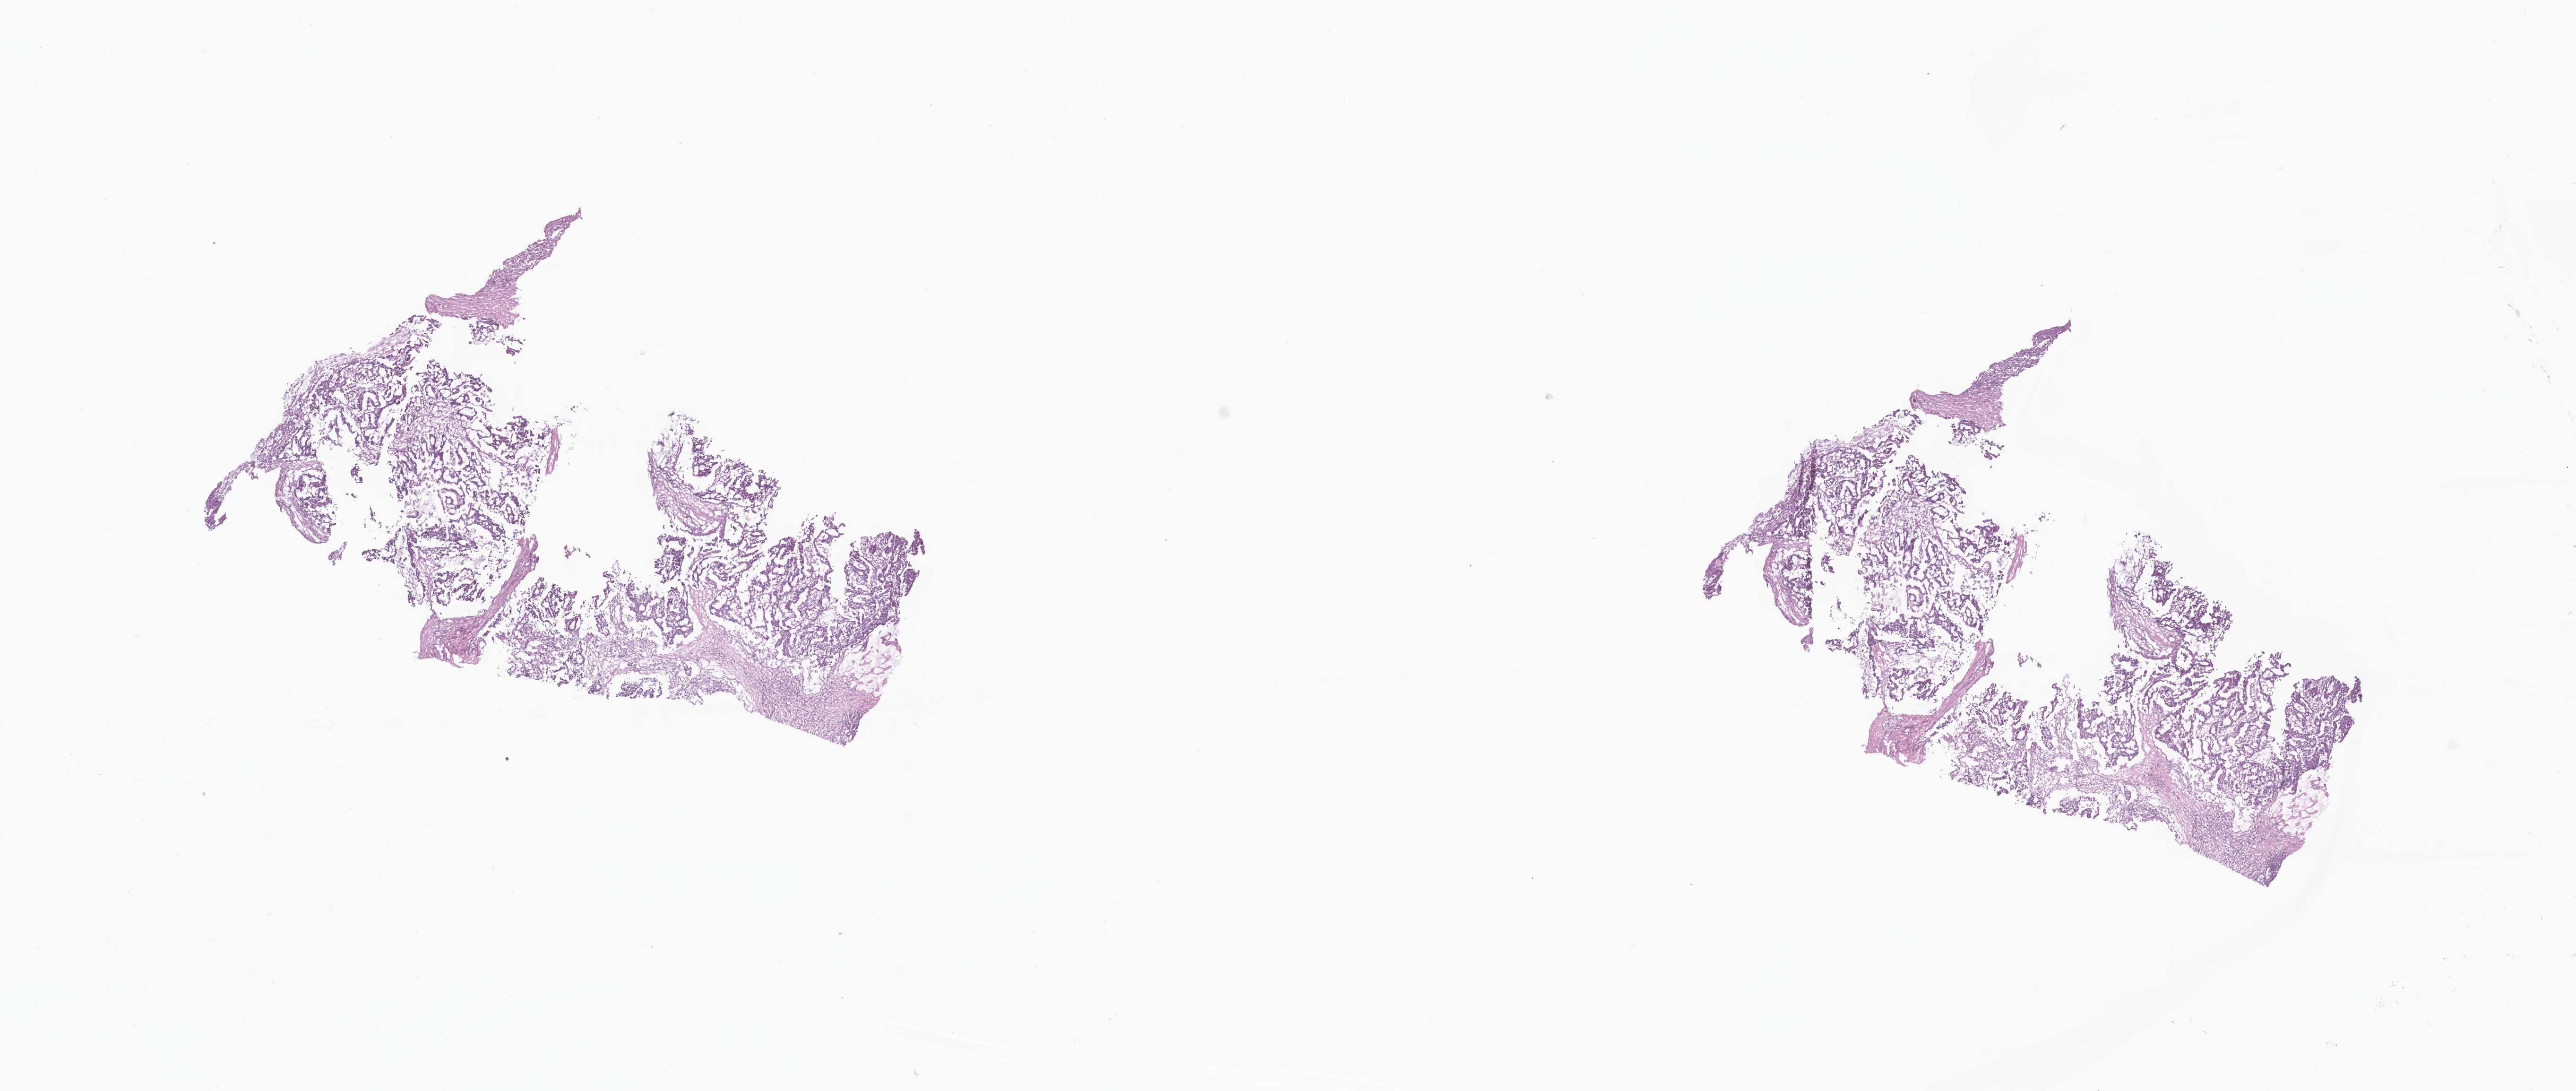
Whole-slide image, hematoxylin and eosin (H&E) stain — shown as a low-resolution overview of the whole scanned area (about 23.0 x 9.7 mm). Frozen section. Specimen: metastatic tumor tissue, resected from liver. Patient: male, age at initial diagnosis 84 years. Composition of this section per pathologist review: tumor cells 80%, tumor nuclei 80%, stromal cells 18%, necrosis 2%, normal cells 0%. Infiltration values recorded for this section: lymphocyte infiltration 3%, monocyte infiltration 4%, neutrophil infiltration 6%.
- section: top of the tissue portion
- patient diagnosis (primary): Adenocarcinoma, NOS